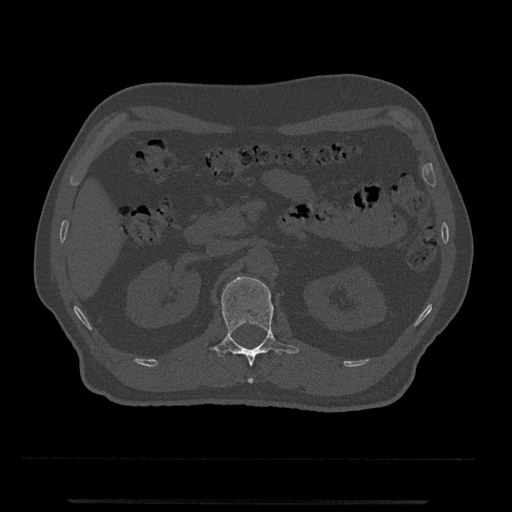
CT including the spine, one axial slice; position 334 of 797 along the scan axis; reconstruction kernel Br40s/3; 120 kVp; bone window (W 1800 / L 400 HU); 0.5 mm slice thickness; 512 × 512 image matrix, field of view 419 × 419 mm. Patient: male, 63 years. Case-level facts recorded for this patient, not image findings: primary cancer: prostate.
Outlined on this slice (semi-automatically segmented with operator editing):
- L1 vertebra: box from (x=210, y=276) to (x=299, y=383) px